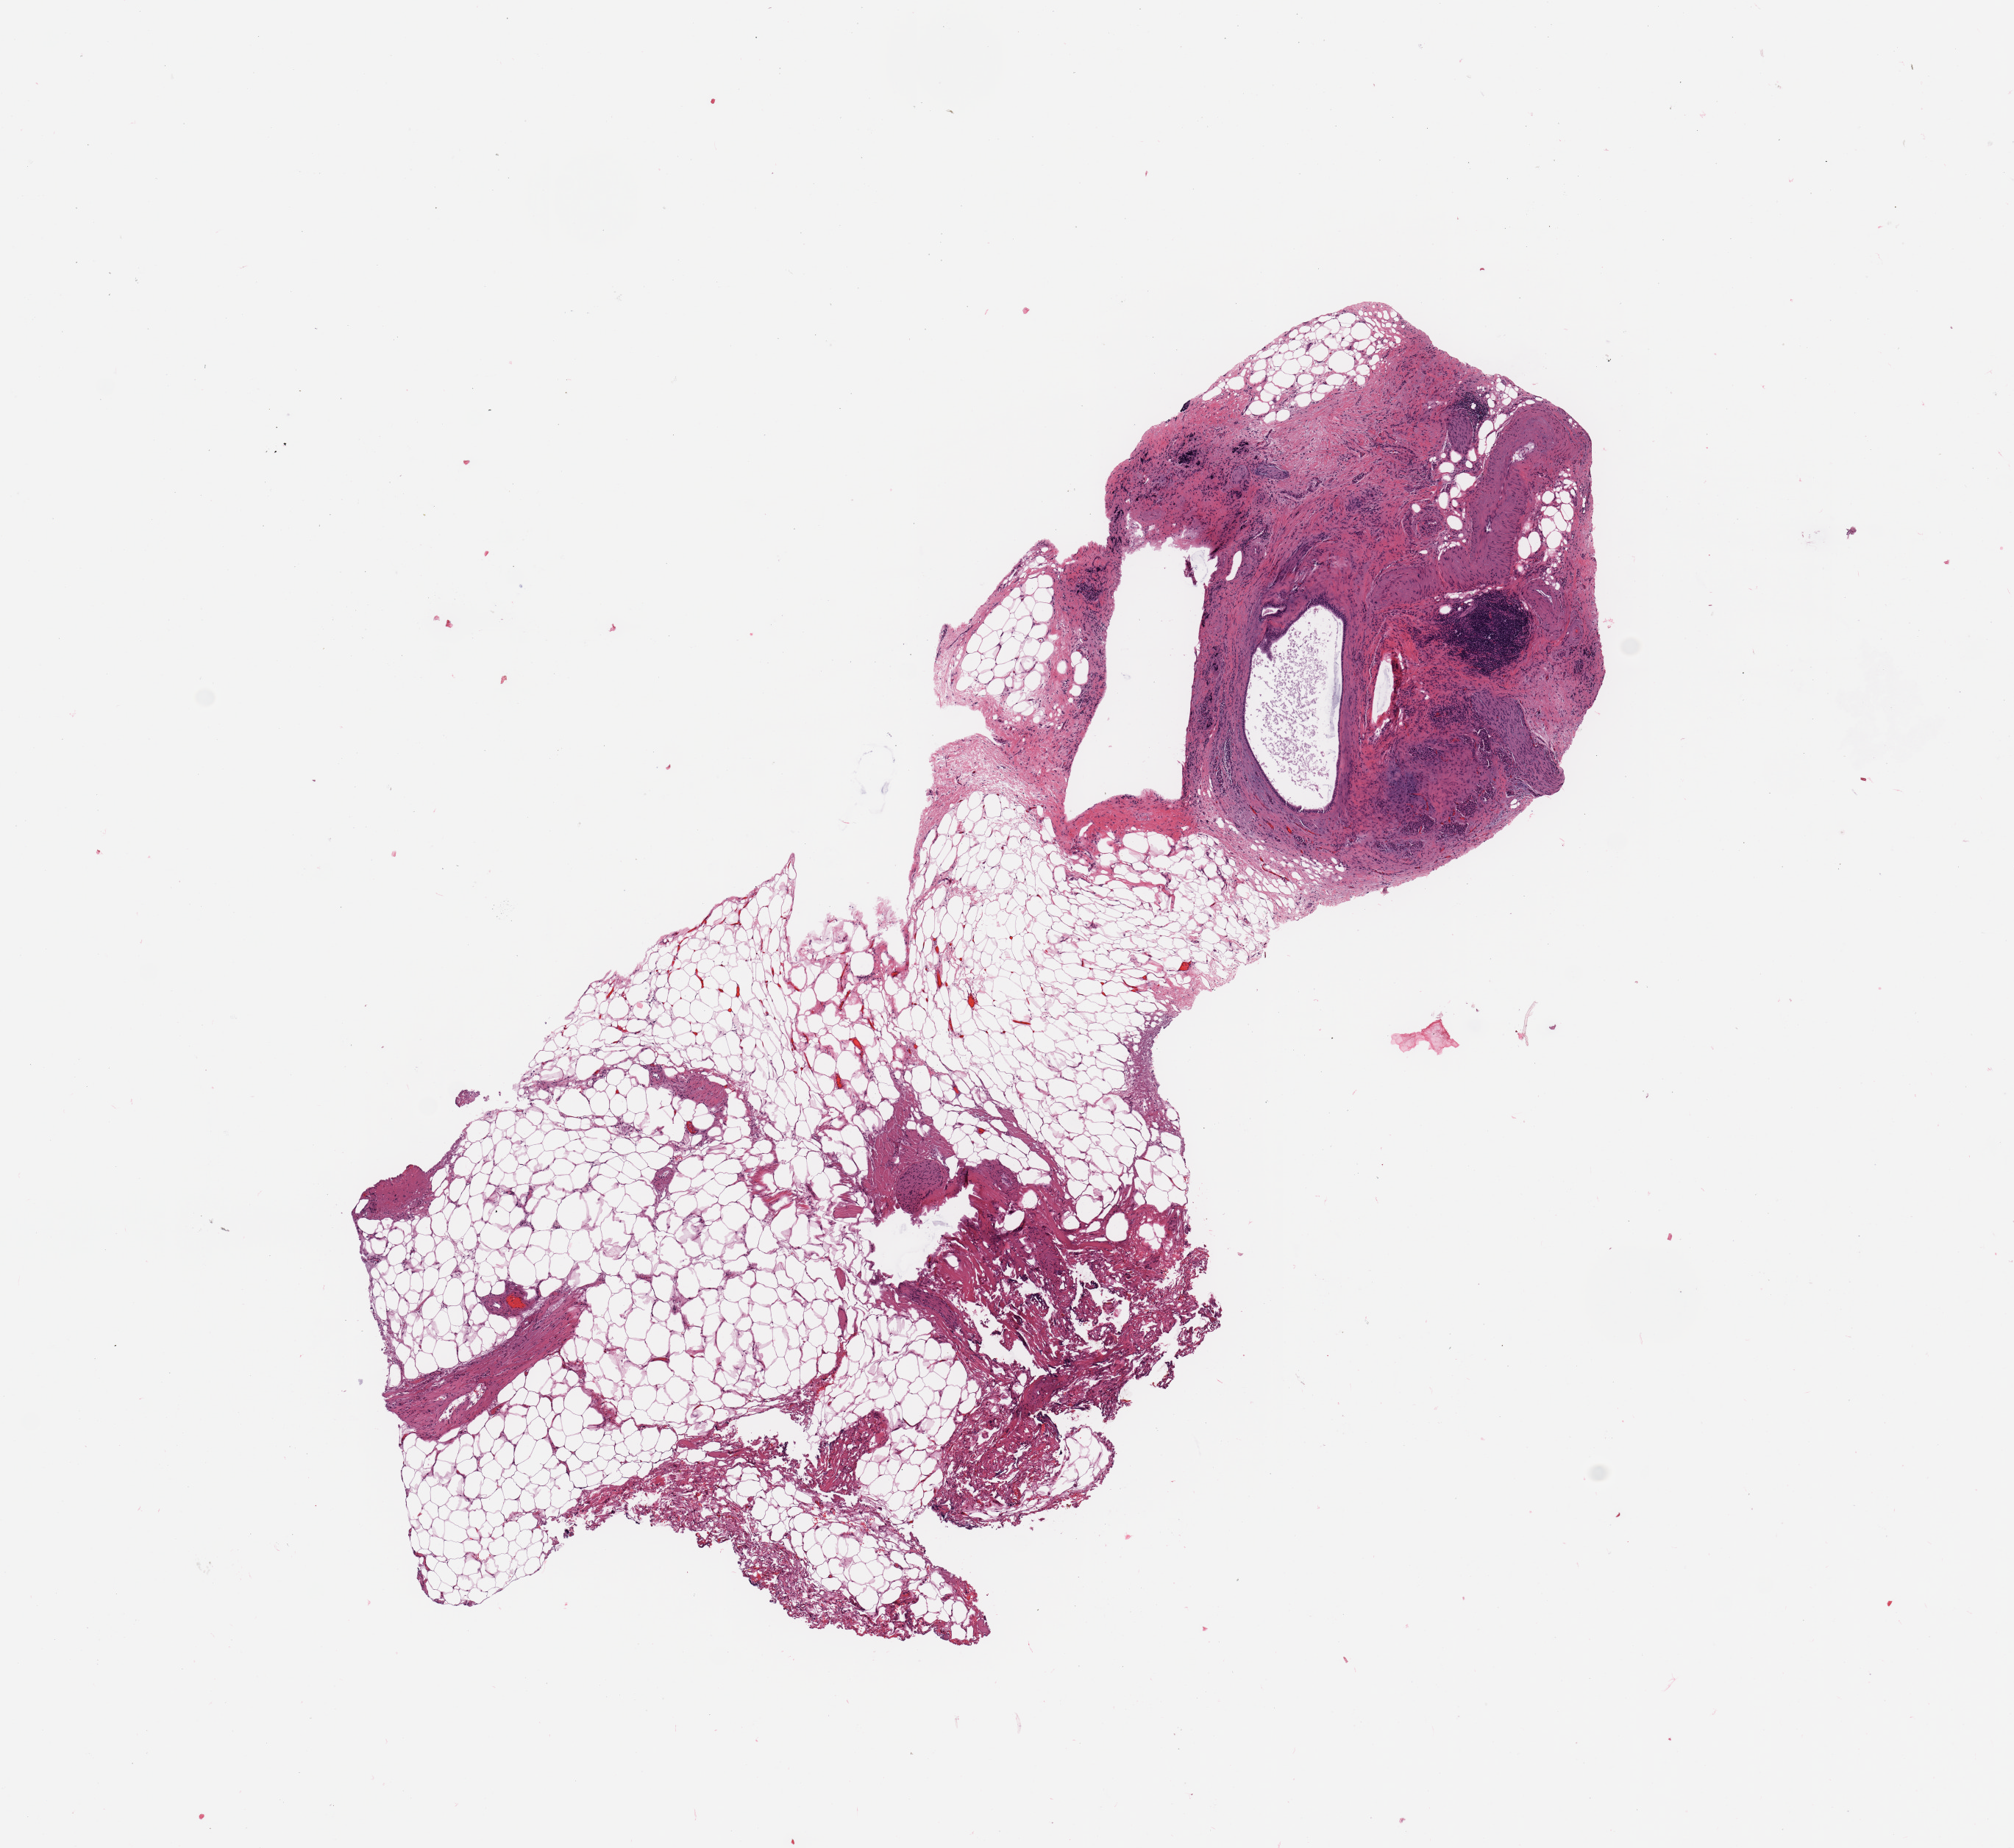
Digitized Hematoxylin and eosin (H&E) stained tissue section (whole slide), a low-resolution overview of the entire scanned area, about 10.8 x 9.9 mm. Normal (non-tumour) tissue sample, pancreas. 84-year-old male patient.
• this section: normal (non-tumour) tissue from the same patient
• patient diagnosis: Infiltrating duct carcinoma, NOS